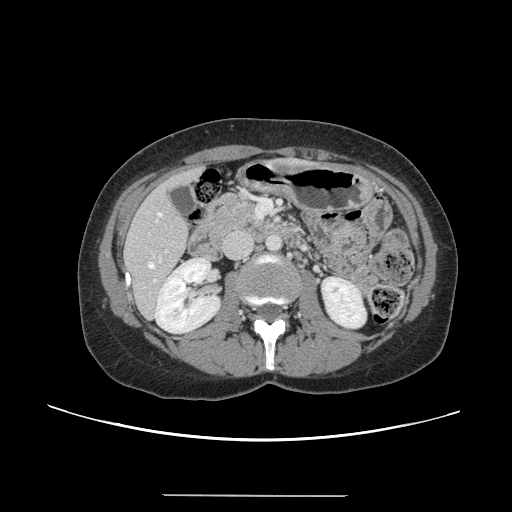
Contrast-enhanced abdominal CT, one axial slice. Position 53 of 144 along the scan axis. 120 kVp. Intravenous contrast given. Soft-tissue window (W 400 / L 40 HU). 512 × 512 image matrix, field of view 380 × 380 mm. Female patient, age 53 years. Case-level facts recorded for this patient, not image findings: diagnosis: colorectal cancer liver metastases, imaged before liver resection; multiple liver metastases: yes; largest metastasis: 1.1 cm; chemotherapy before resection: no.
Annotated regions visible in this slice (expert manual segmentation):
- hepatic veins: bounding box [x1, y1, x2, y2] px = [148, 212, 161, 268]
- liver: [125, 168, 203, 317]
- planned liver remnant (the part of the liver to remain after resection): [125, 168, 203, 313]
- portal vein (with intrahepatic branches): [153, 250, 168, 283]